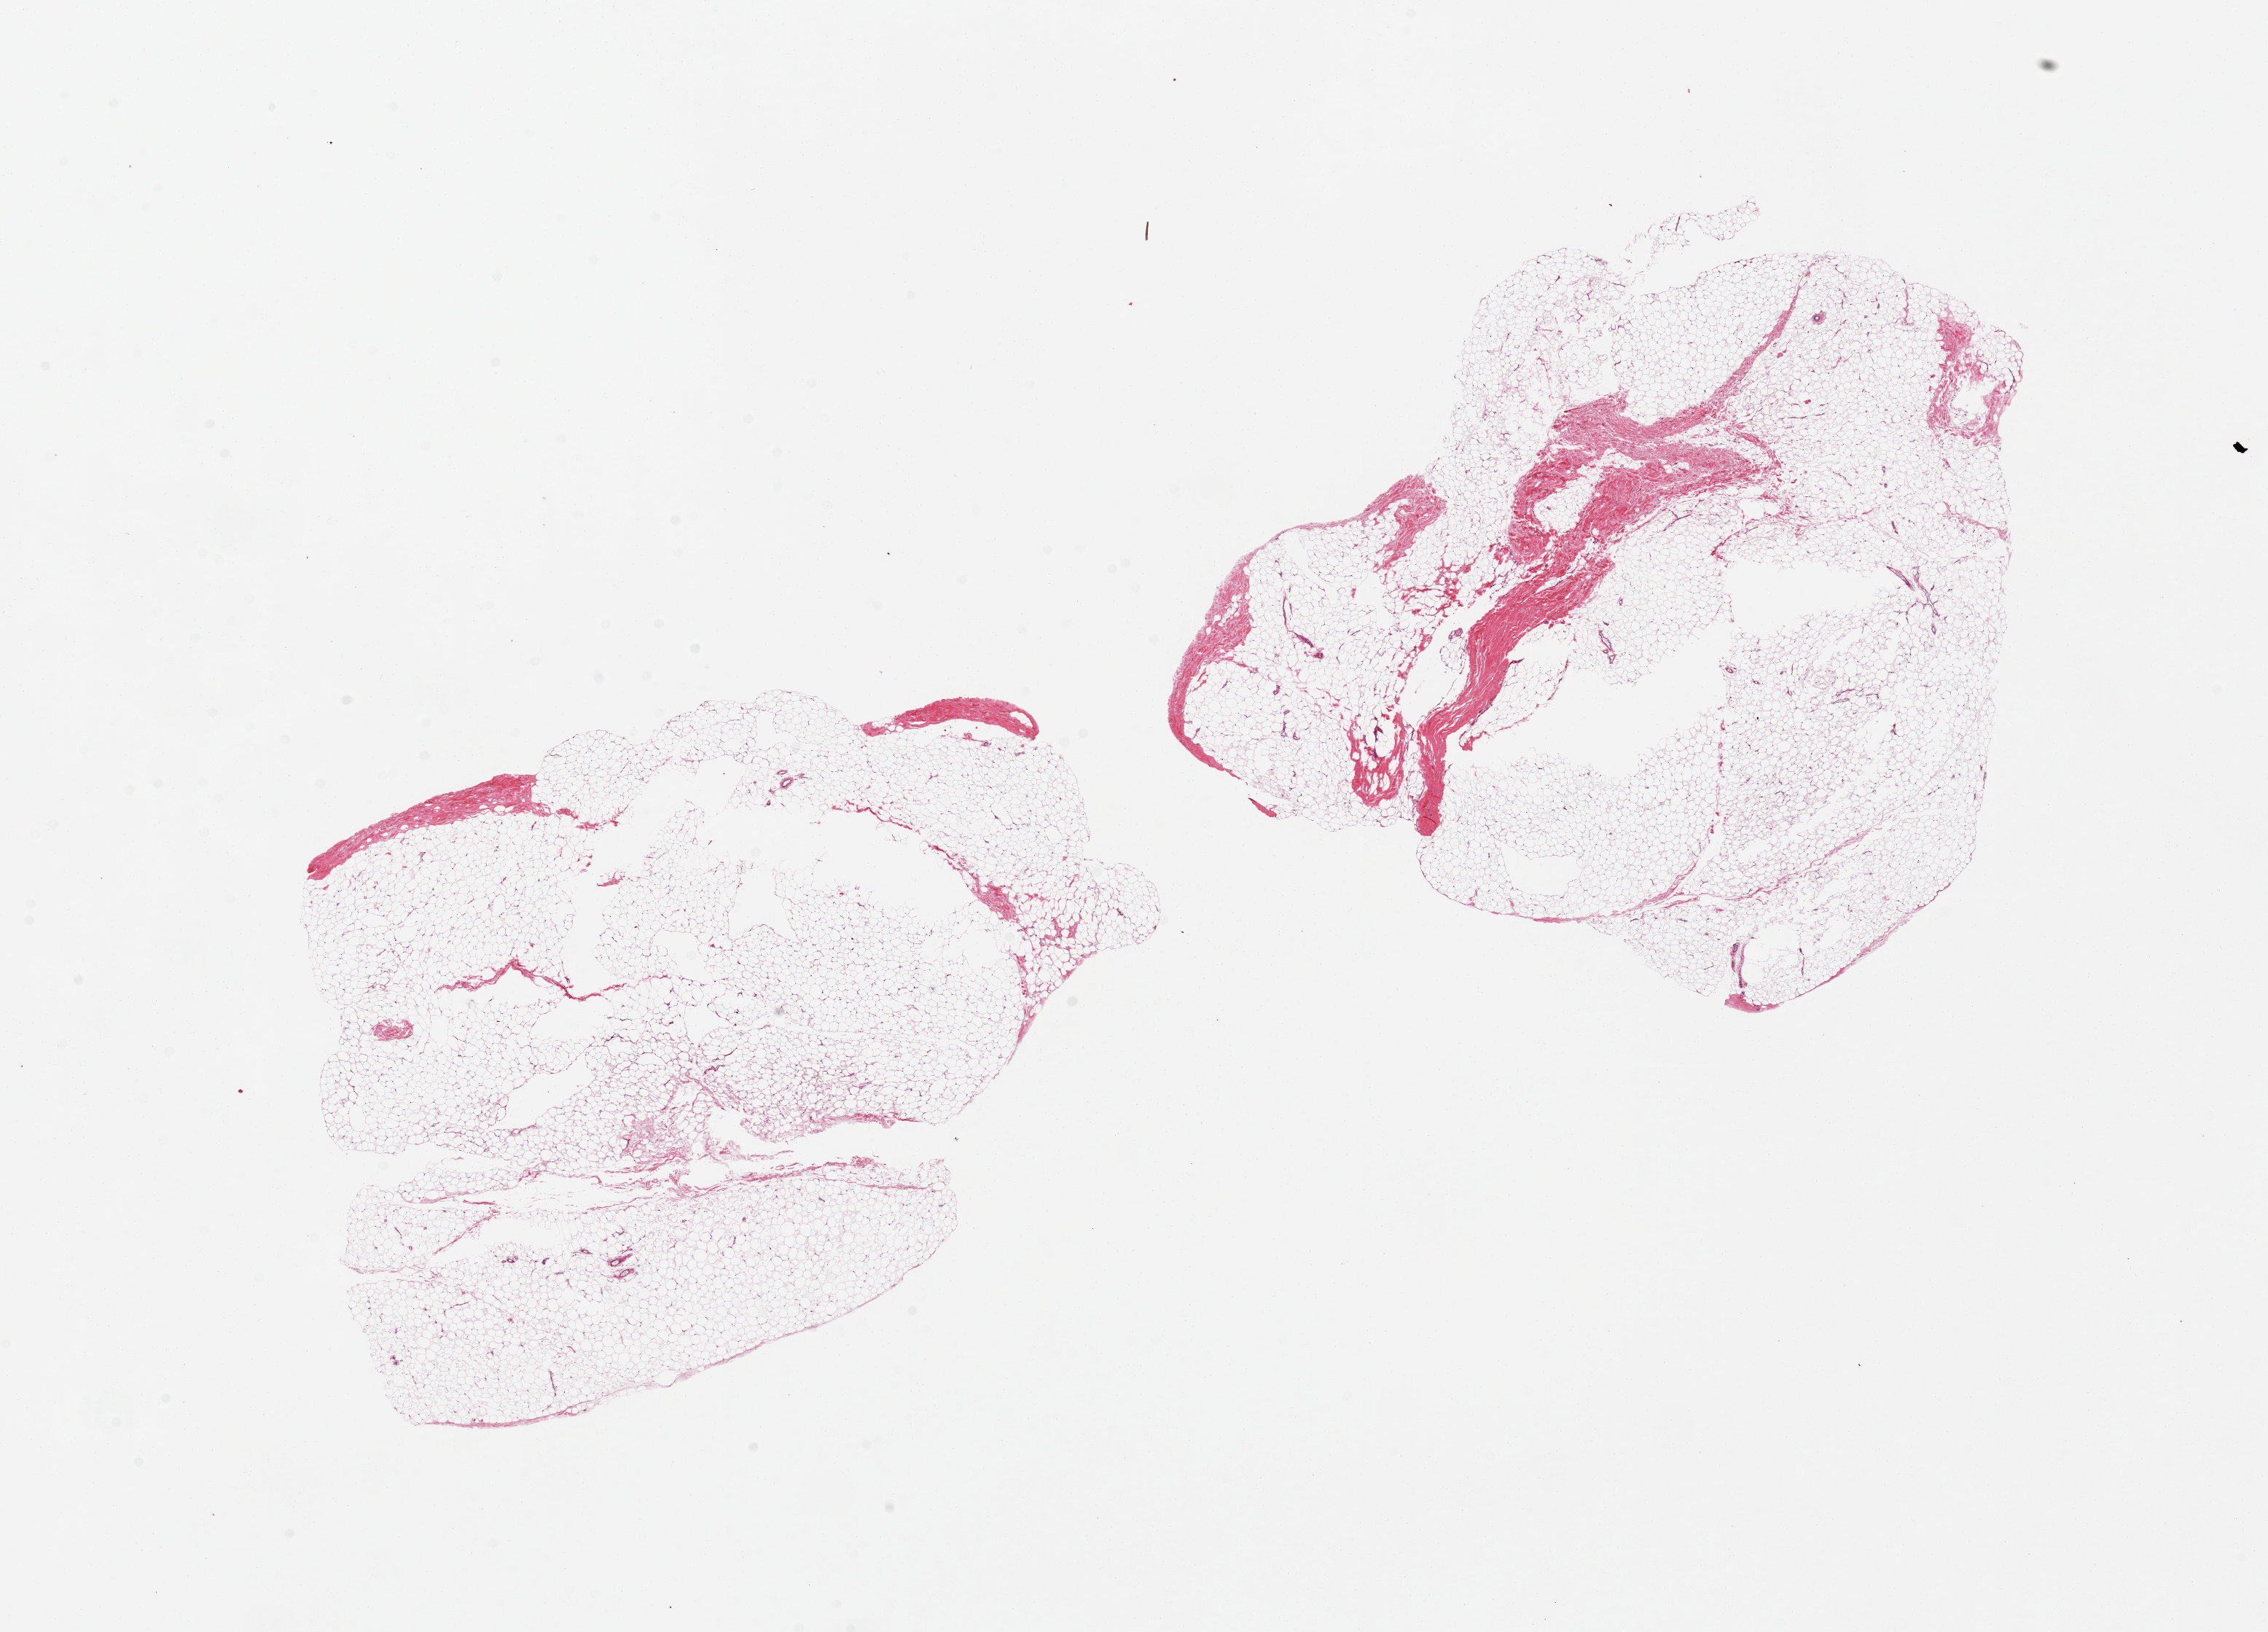
Whole-slide image, hematoxylin and eosin (H&E) stain, low-resolution overview of the scanned area, about 24.6 x 17.7 mm (slide scanned at 20x), PAXgene-fixed, paraffin-embedded tissue, target tissue: breast, tissue donor sample. Male donor.
Pathologist's review note for this sample: 2 pieces, 10x7 & 10x8mm; no ducts, all adipose, several holes.